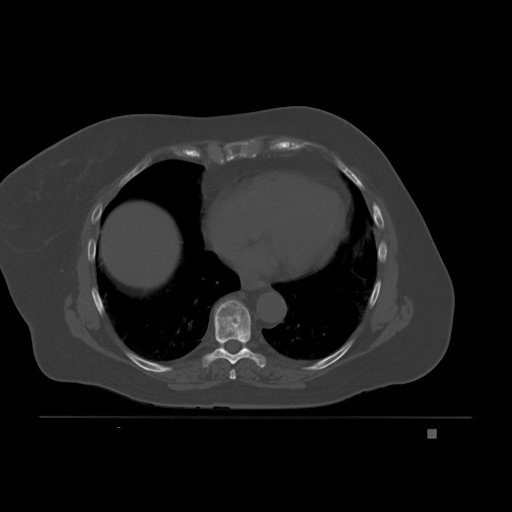
CT including the spine, one axial slice; bone window (W 1800 / L 400 HU); 512 × 512 image matrix, field of view 474 × 474 mm. Patient: female, 63 years. From the clinical record (not read from this slice): primary cancer: breast.
Annotated regions visible in this slice (semi-automatically segmented with operator editing):
- T7 vertebra: box from (x=229, y=369) to (x=236, y=380) px
- T8 vertebra: (x=202, y=300)–(x=266, y=368)